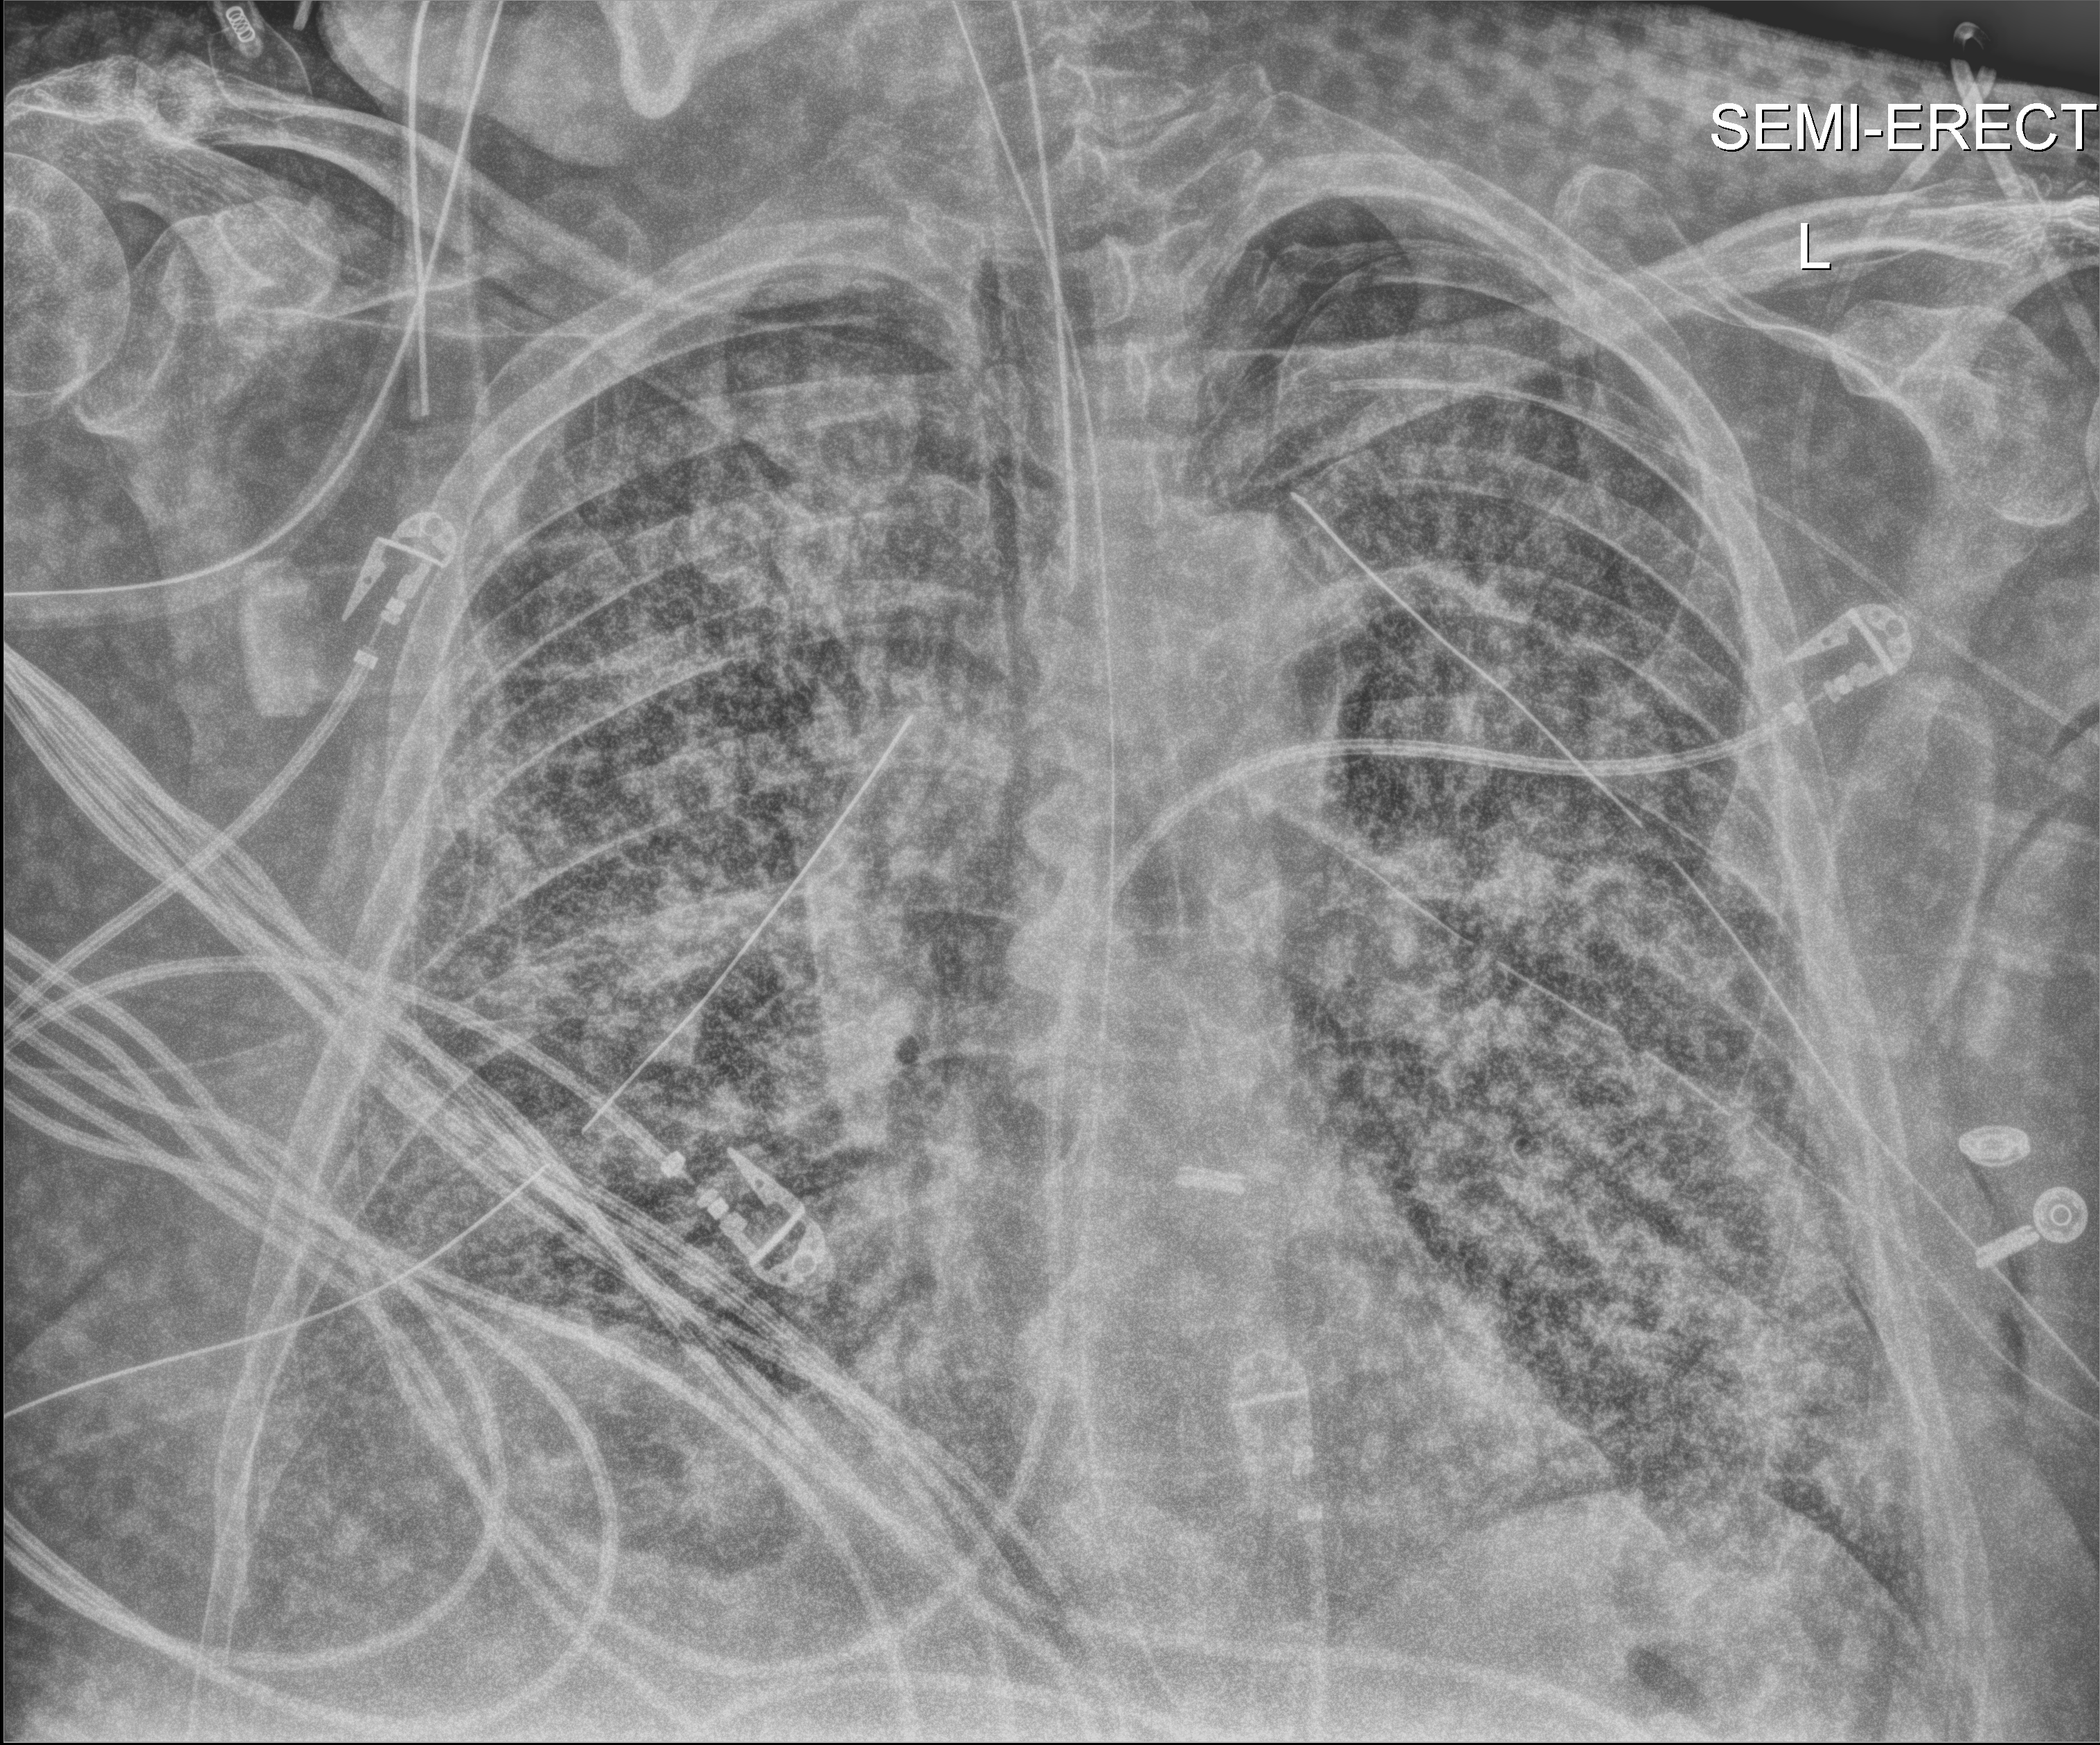
Bedside chest radiograph (digital radiography). Patient hospitalised with COVID-19, aged 18–59 years.
Admission-level facts for this patient (not findings on this image; timing relative to this image not recorded): smoking status (admission record): never.